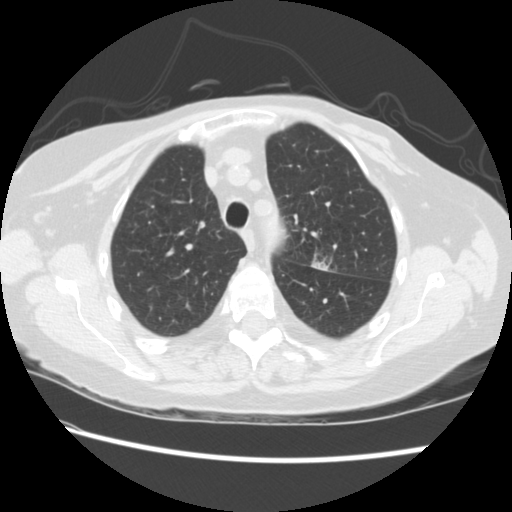
Low-dose screening chest CT, one axial slice. Slice 165 of 224 in the series (ordered by position). Reconstruction kernel STANDARD. Lung window (W 1500 / L -600 HU). 512 × 512 image matrix, field of view 340 × 340 mm.
Outlined on this slice (manually delineated by an expert):
- lesion 1 (tumor, upper lobe of left lung): box from (x=313, y=261) to (x=328, y=271) px